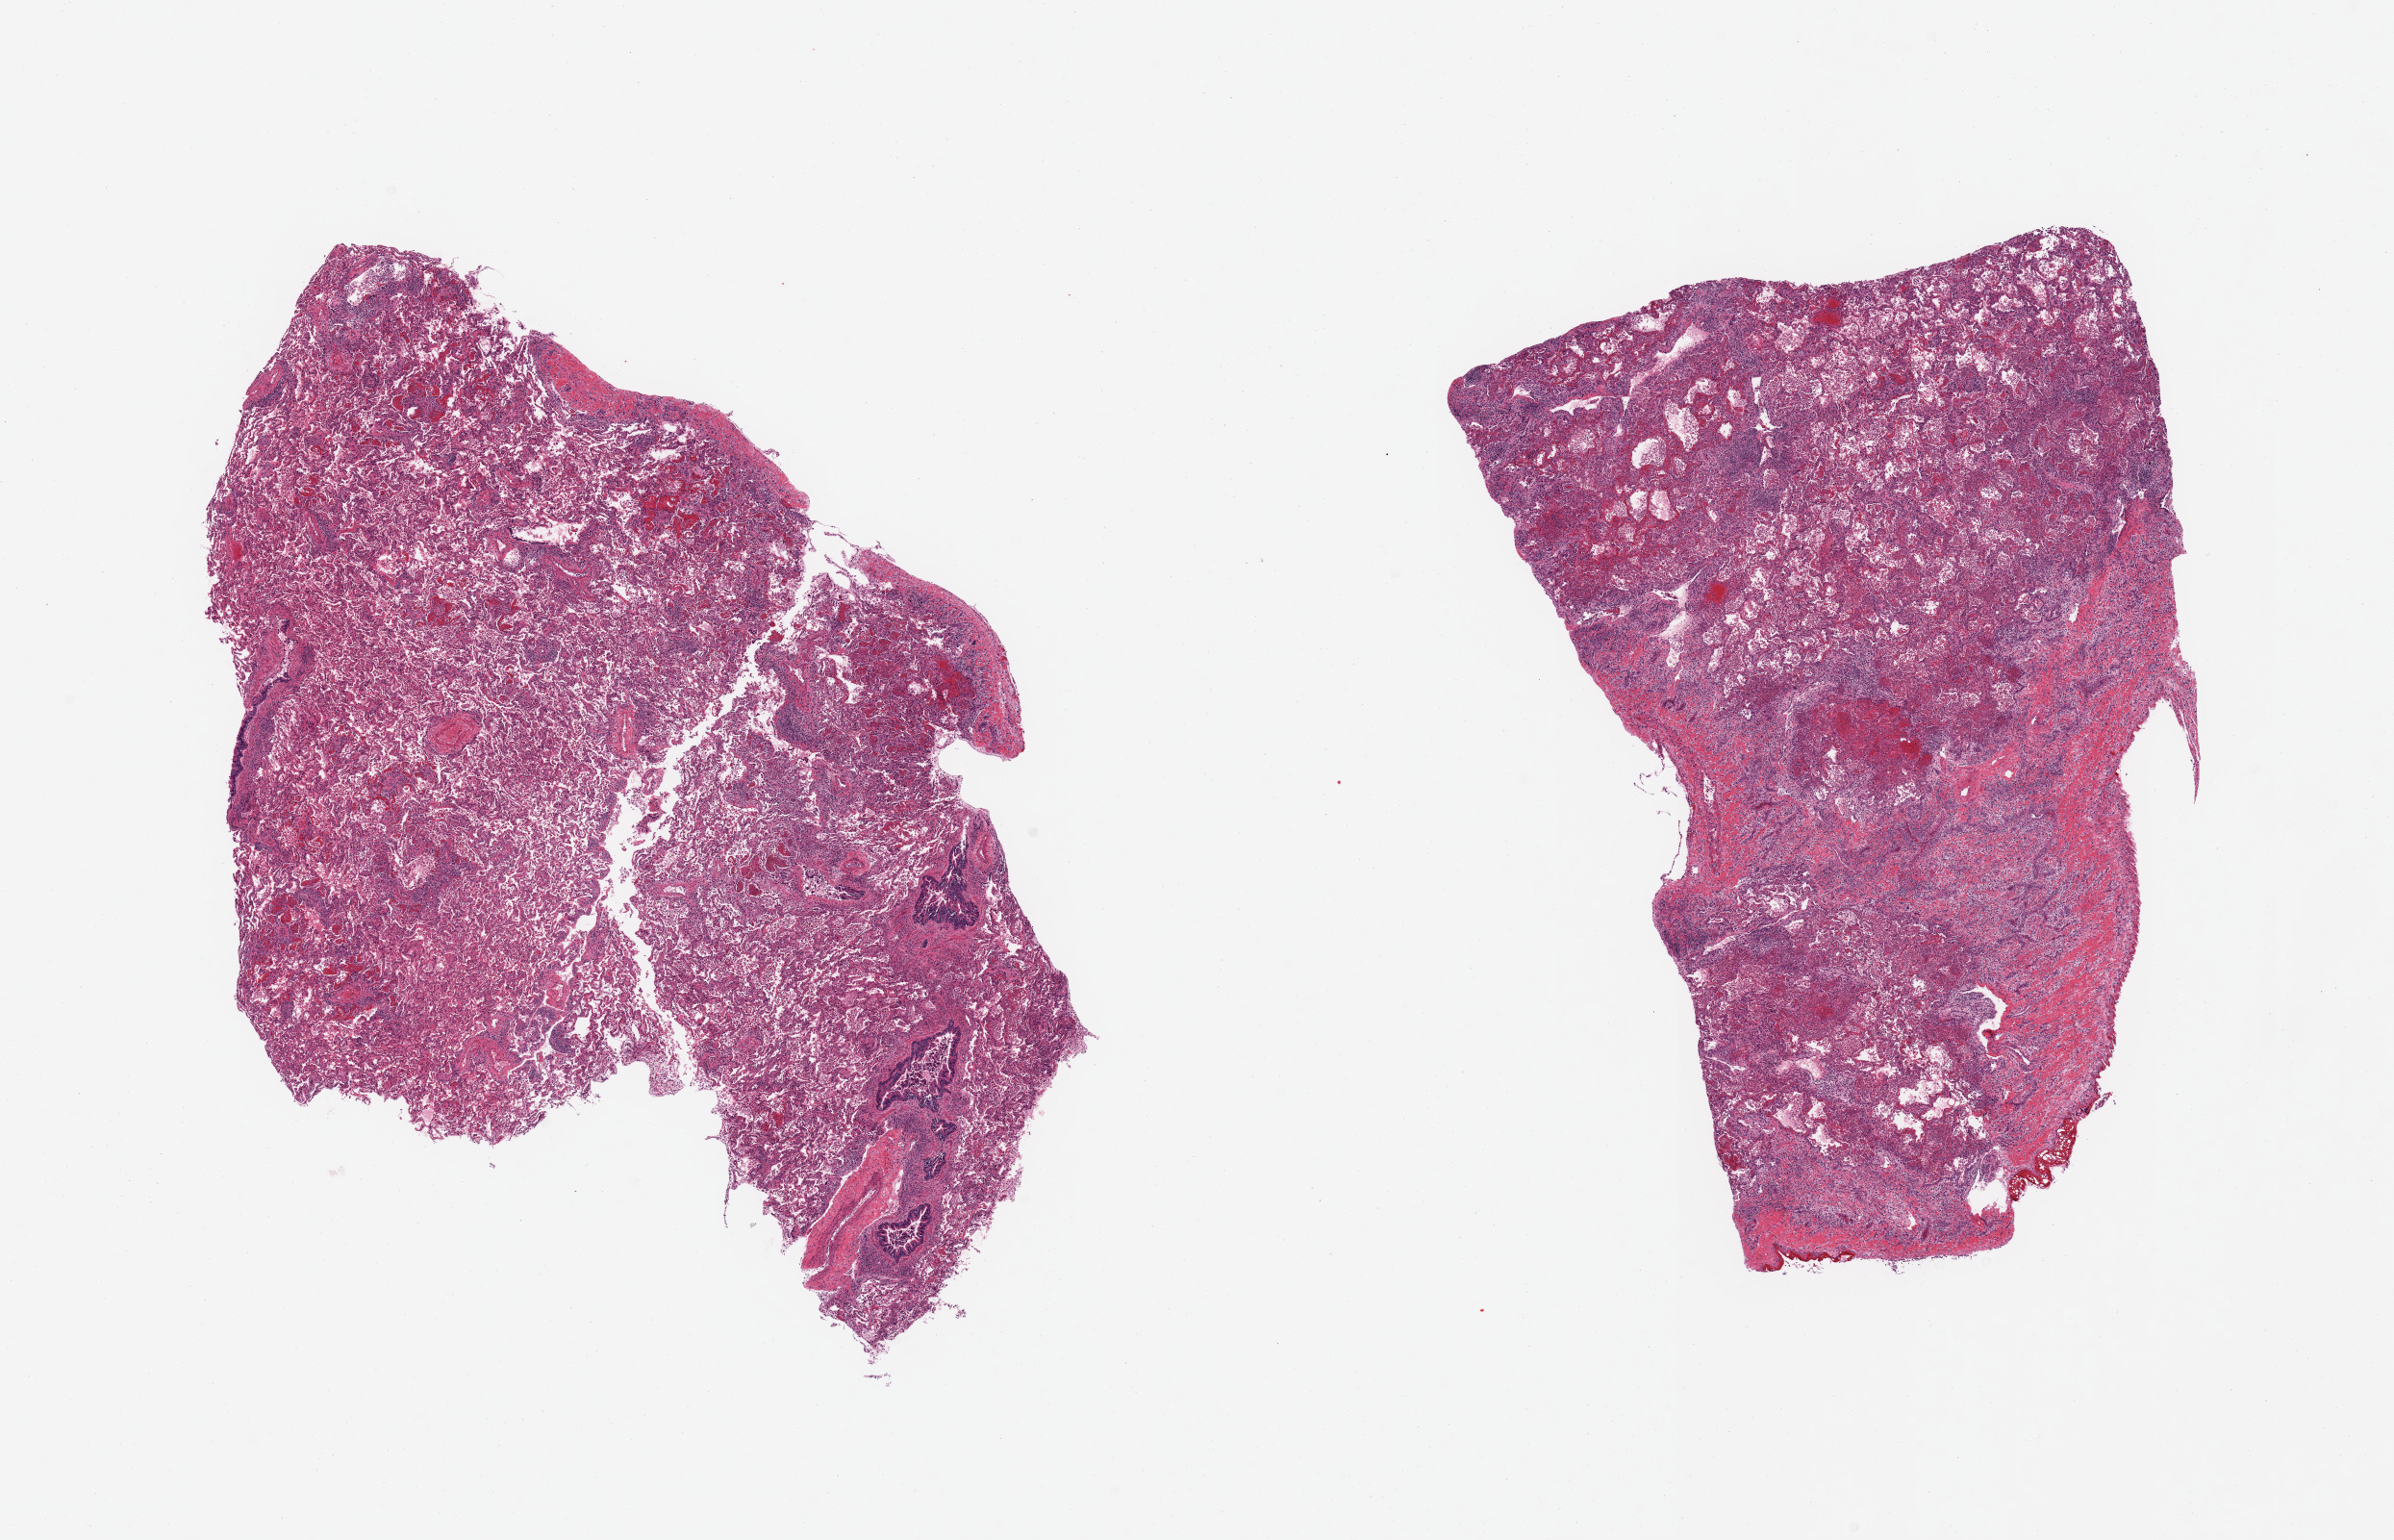
Whole-slide image, hematoxylin and eosin (H&E) stain, brightfield, shown as a low-resolution overview of the whole scanned area (about 19.7 x 12.7 mm, acquisition: 20x scan); PAXgene-fixed, paraffin-embedded tissue; target tissue: lung; donor tissue sample.
- review note (as recorded): 2 pieces; massive pneumonia; marked congestion